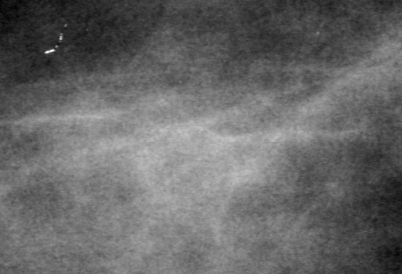
Cropped region of a digitized screen-film mammogram centred on a radiologist-marked abnormality; right breast; CC view.
Finding: mass, shape lobulated, margins obscured; BI-RADS assessment category 3; subtlety rating 4 on a 1 (subtle) to 5 (obvious) scale; pathology (as recorded): benign.